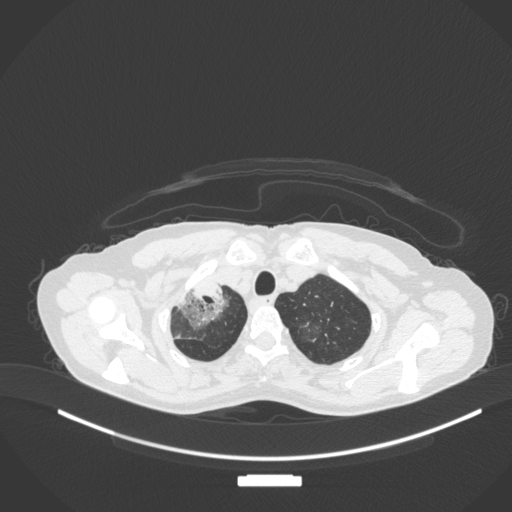
Chest CT, one axial slice; position 286 of 311 along the scan axis; reconstruction kernel B31f; 120 kVp; lung window (W 1500 / L -600 HU); 512 × 512 image matrix, field of view 400 × 400 mm. Patient: female, 59 years. Case-level facts recorded for this patient, not image findings: clinical TNM (as recorded): T3 N0 M0; histopathological grade: G1.
Outlined on this slice (rectangle marked by the reading radiologist):
- lung tumour (recorded histology: adenocarcinoma): bounding box [x1, y1, x2, y2] px = [174, 274, 229, 331]